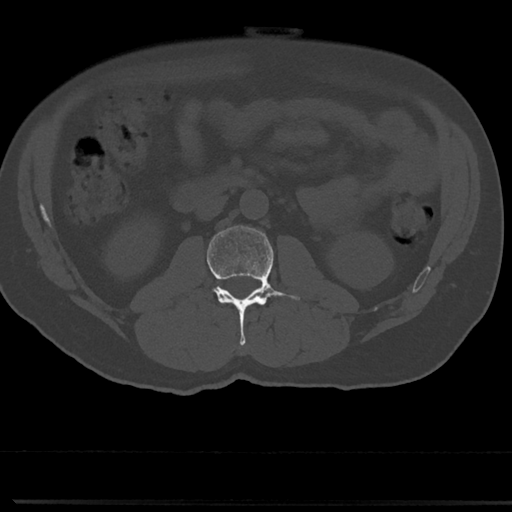
CT including the spine, one axial slice; position 9 of 817 along the scan axis; reconstruction kernel Br40s/3; 120 kVp; bone window (W 1800 / L 400 HU); 512 × 512 image matrix, field of view 355 × 355 mm. Male patient, age 61 years. Case-level facts recorded for this patient, not image findings: primary cancer: prostate.
Annotated regions visible in this slice (semi-automatically segmented with operator editing):
- L2 vertebra: box from (x=207, y=226) to (x=301, y=345) px